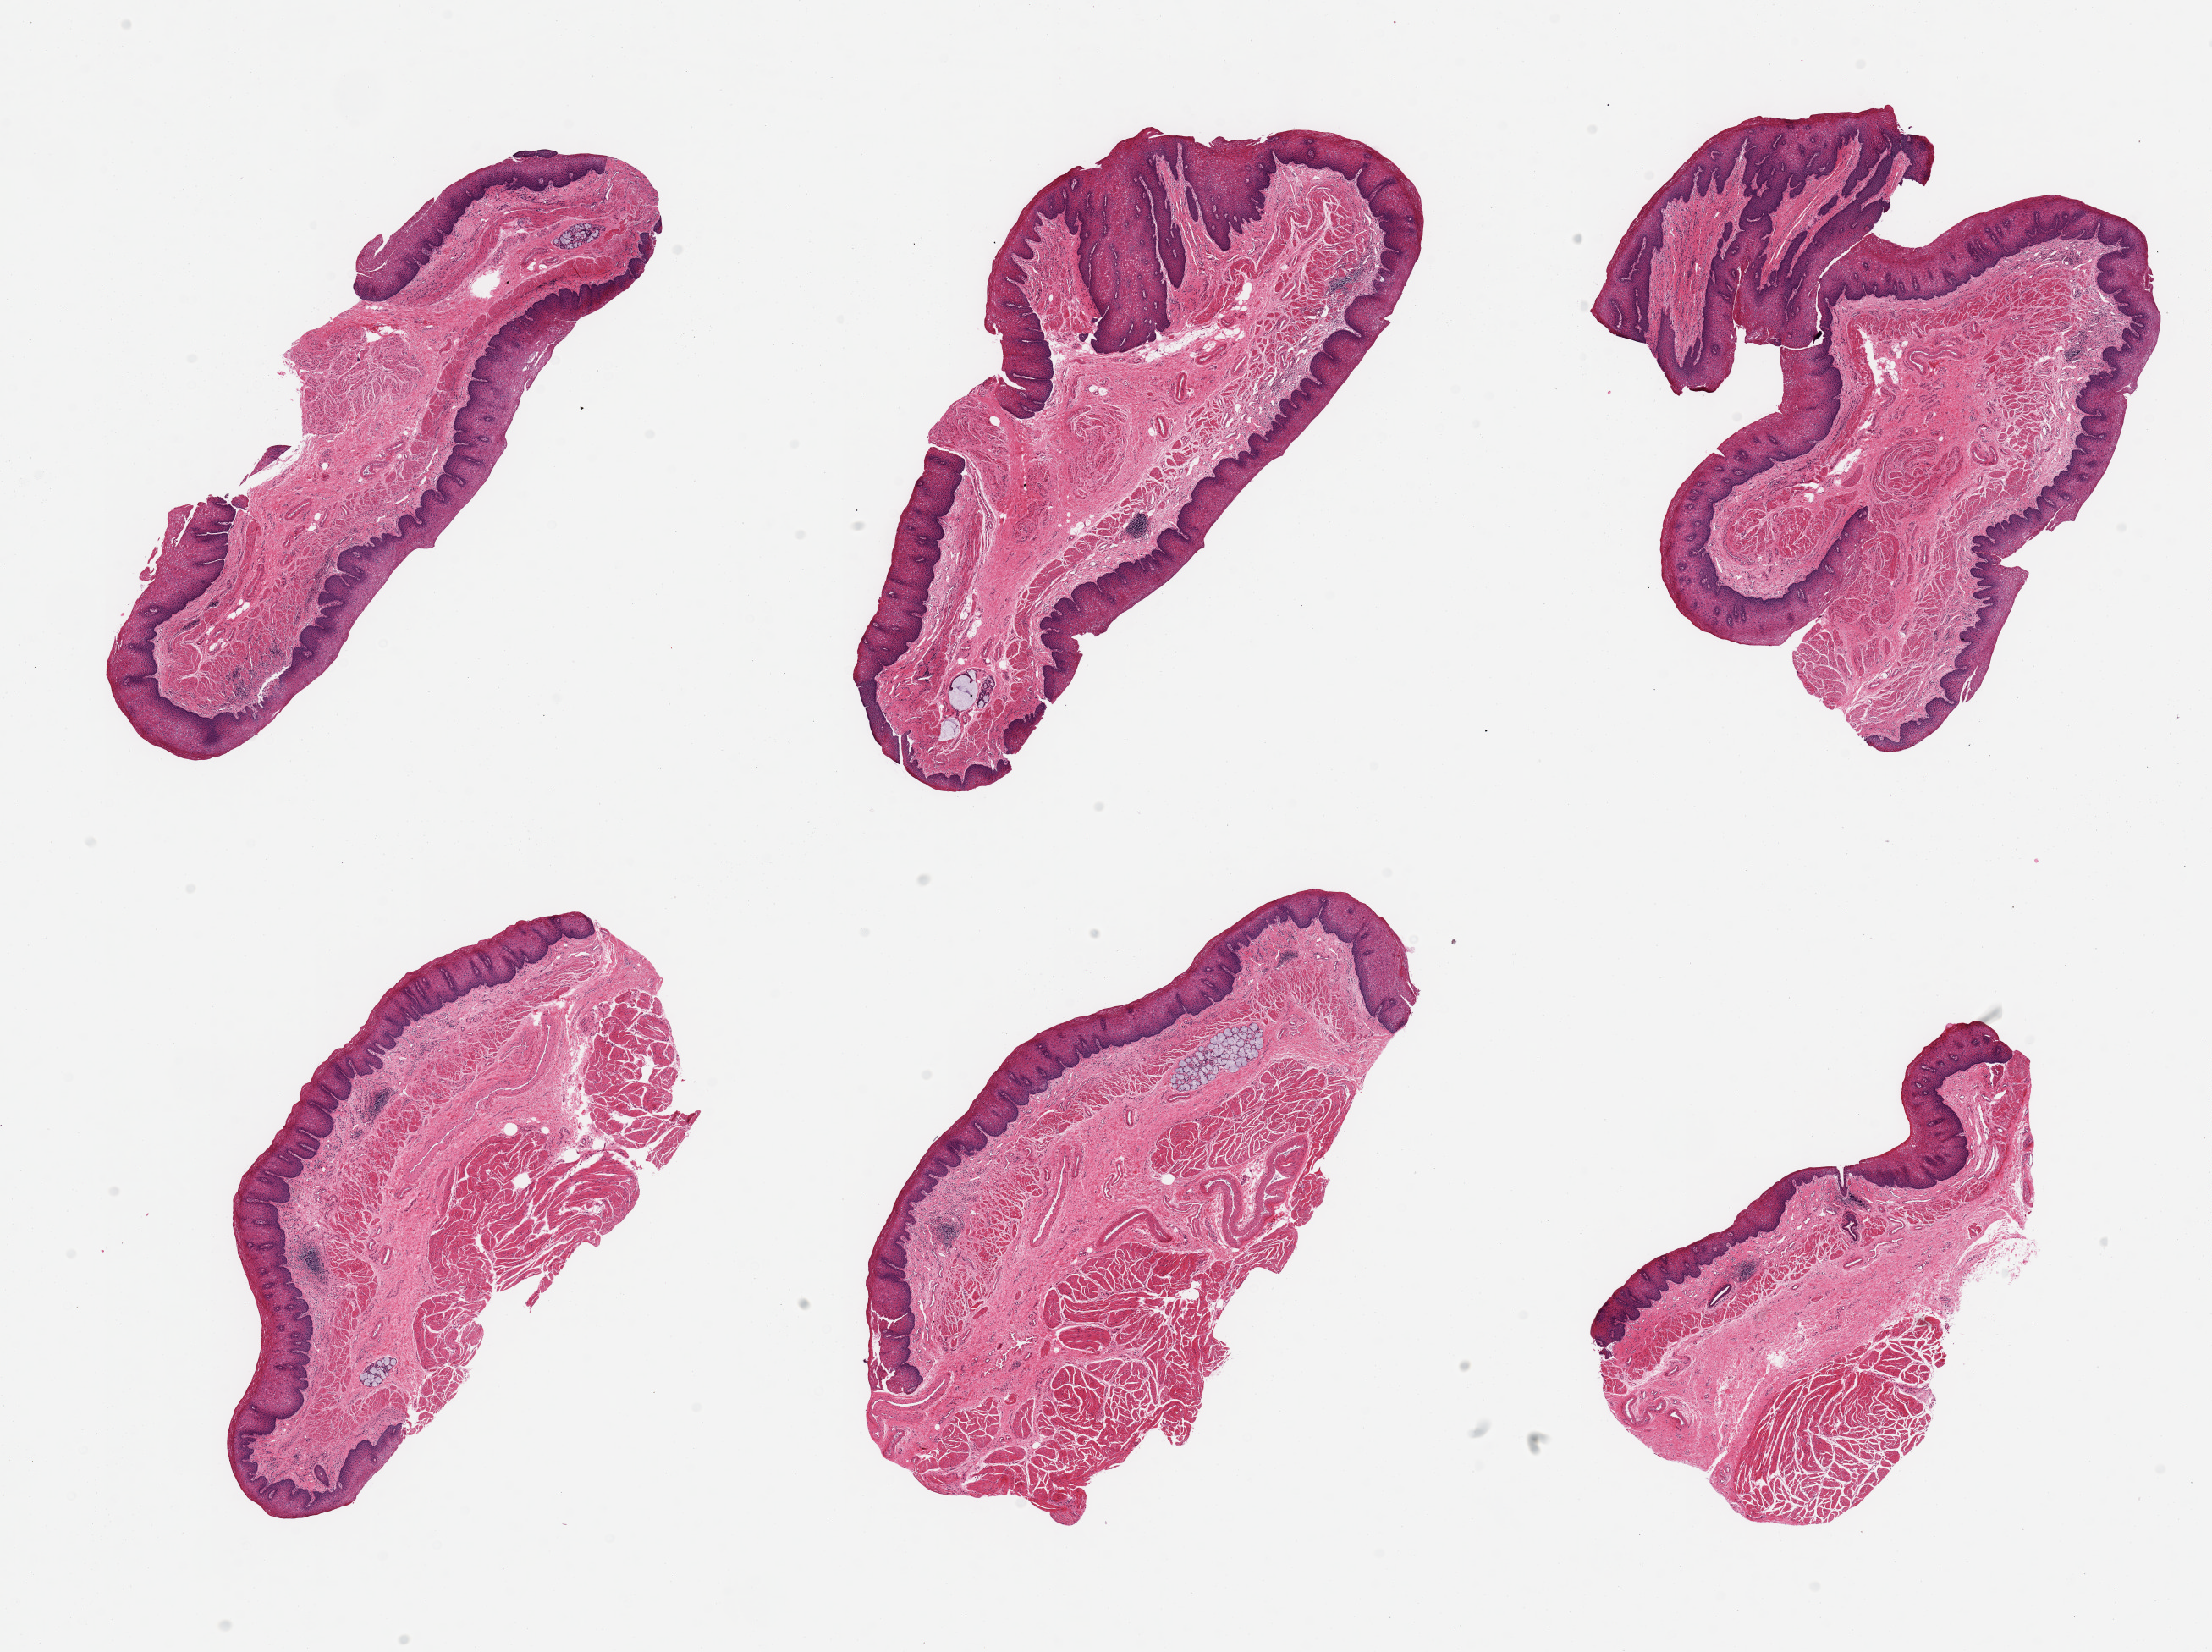
Whole-slide image, haematoxylin and eosin stain, shown as a low-resolution overview of the whole scanned area (about 20.7 x 15.4 mm, from a 20x scan), PAXgene-fixed, paraffin-embedded tissue, sampled site (target tissue): esophageal mucous membrane, tissue donor sample. Donor sex: male.
Review note (as recorded): 6 pieces, squamous mucosa up to ~0.4mm, ~10-20% thickness; Few submucosal mucus glands present.